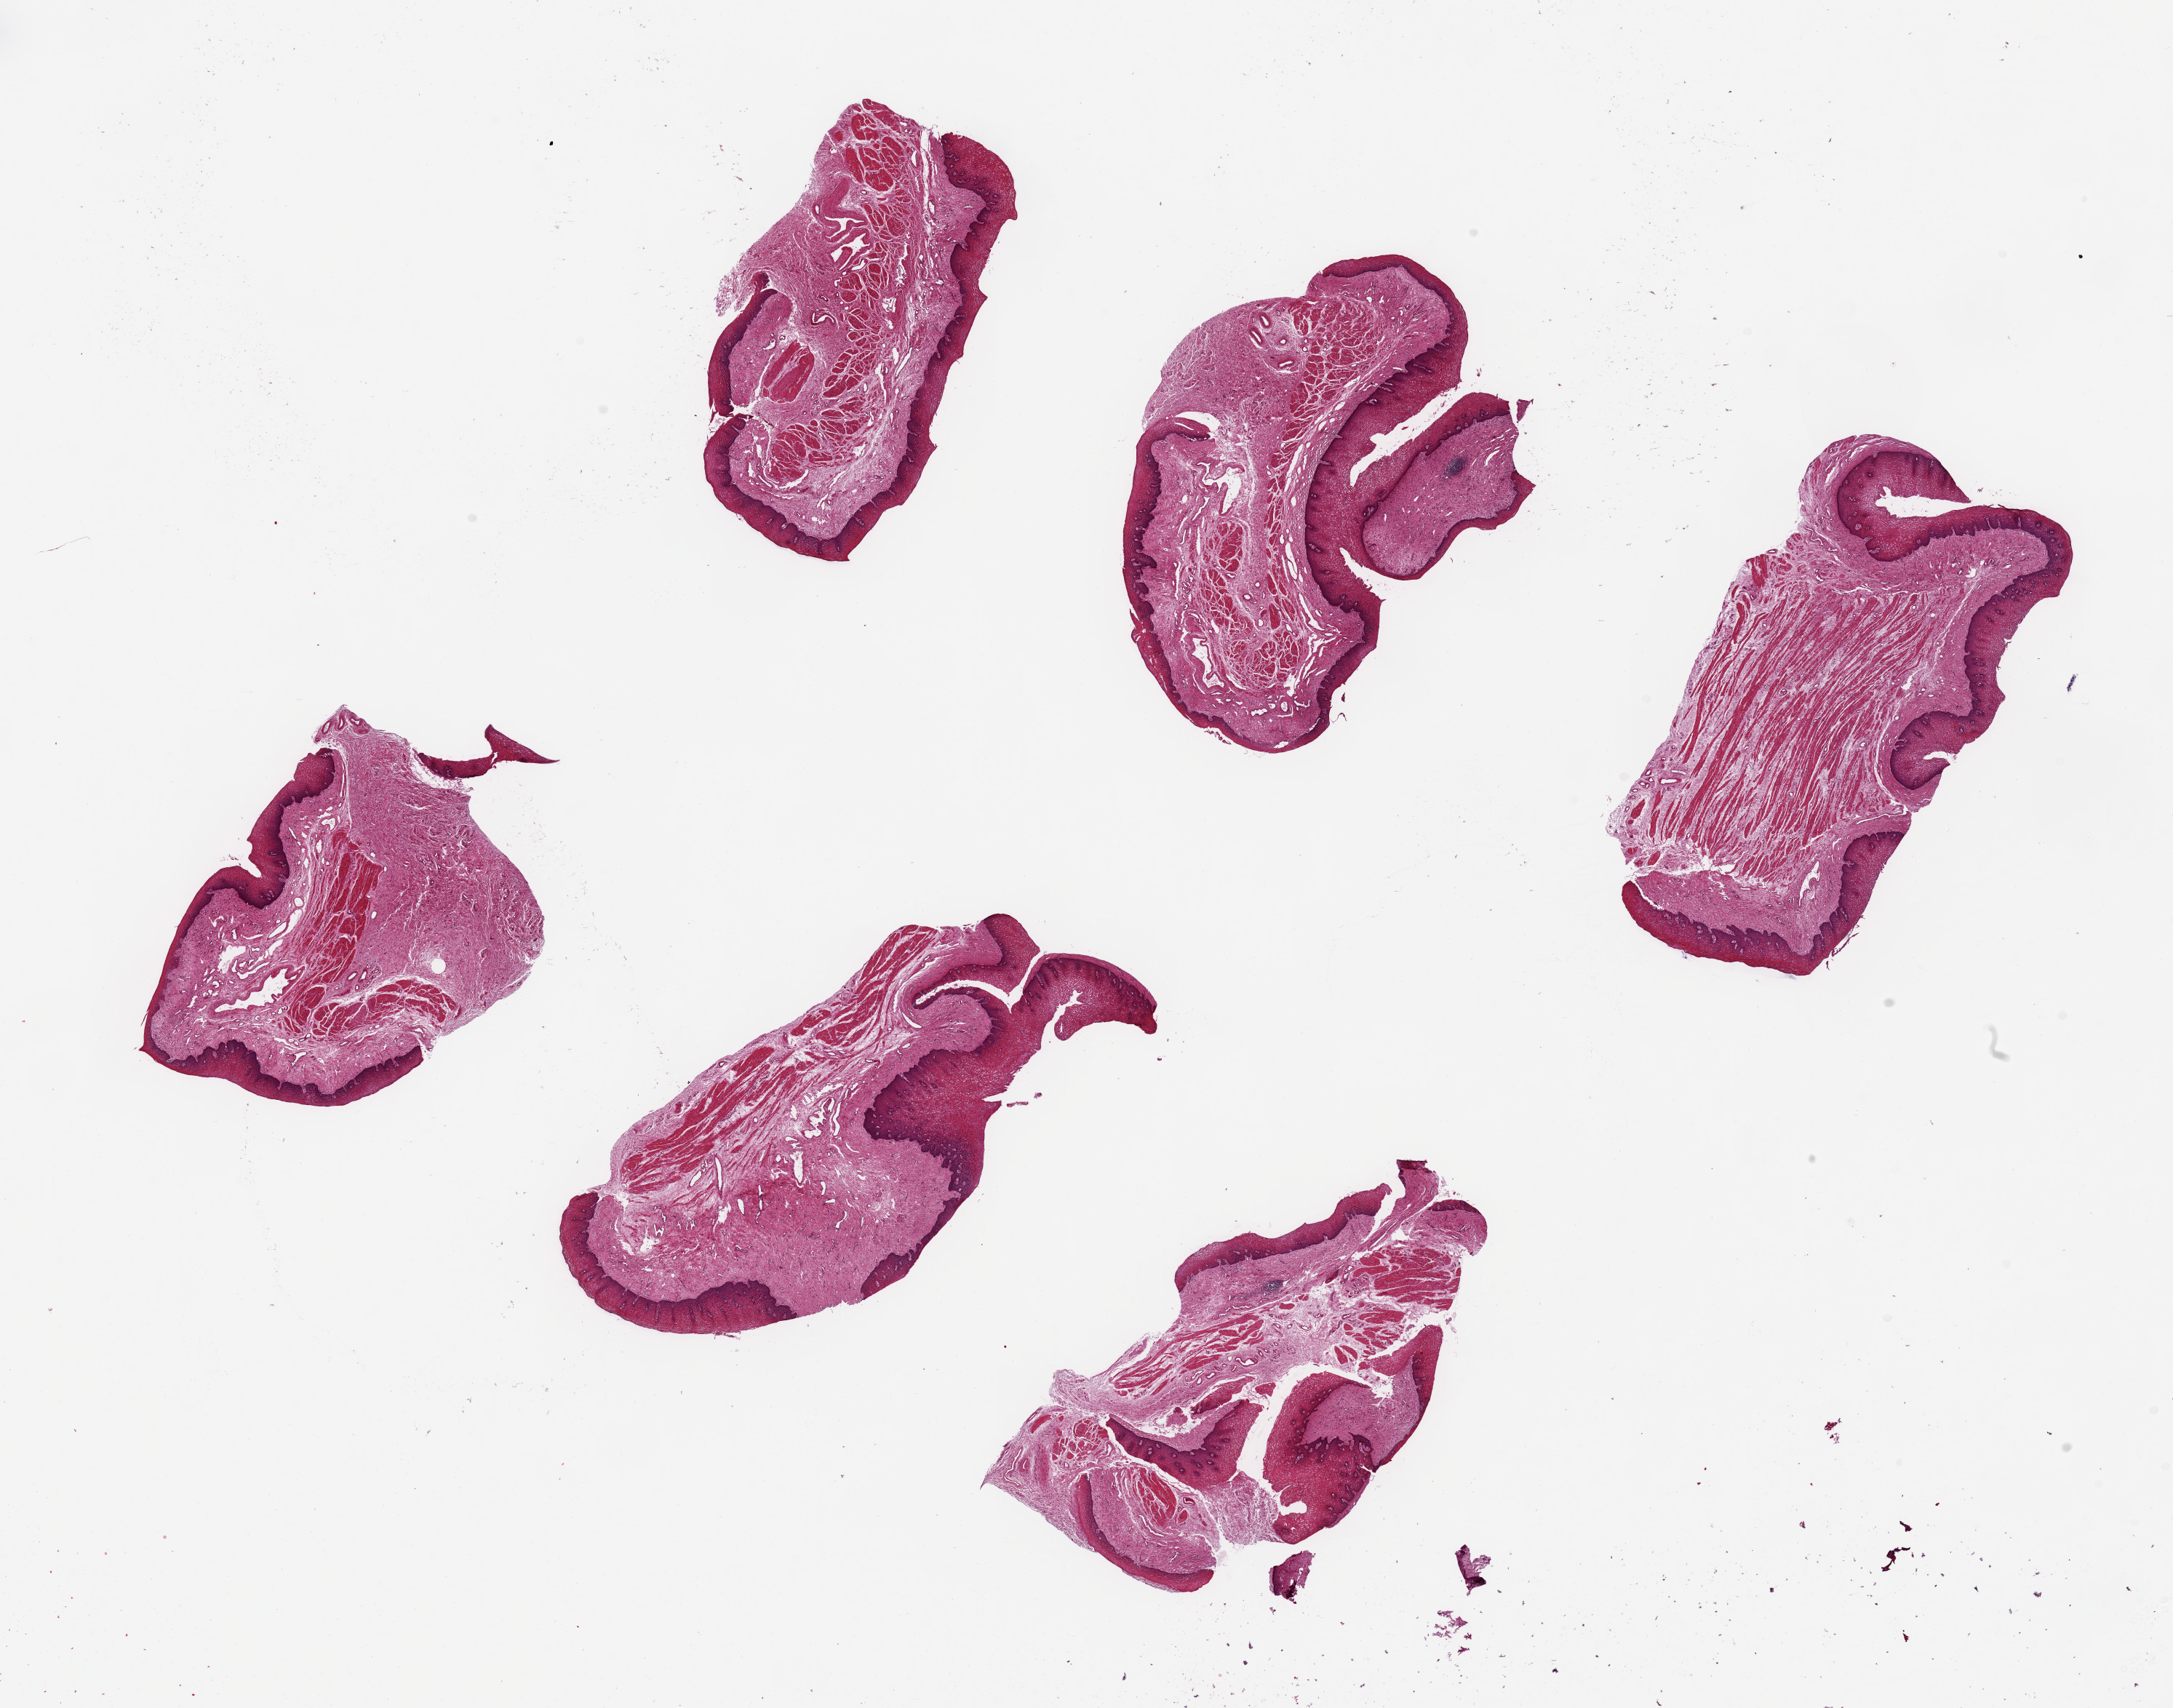
H&E whole-slide image, brightfield — shown as a low-resolution overview of the whole scanned area (about 23.6 x 18.6 mm, slide scanned at 20x). PAXgene-fixed paraffin-embedded (PFPE) section. Target tissue: esophageal mucous membrane. Tissue donor sample. Donor sex: female.
Review note (as recorded): 6 pieces up to 6x3 mm; all are MUCOSA.